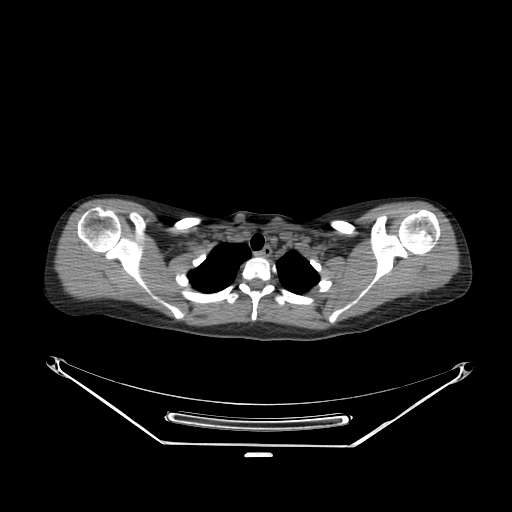
CT of an extremity soft-tissue mass (from a PET/CT study), one axial slice; position 216 of 267 along the scan axis; soft-tissue window (W 400 / L 40 HU); 512 × 512 image matrix, field of view 500 × 500 mm. Female patient. Case-level facts recorded for this patient, not image findings: histological type: malignant fibrous histiocytoma; grade: low; site of the primary tumour: left arm.
Annotated regions visible in this slice (expert contour drawn on MRI and transferred to this co-registered scan by the dataset authors):
- gross tumour volume (mass): box from (x=425, y=272) to (x=432, y=277) px